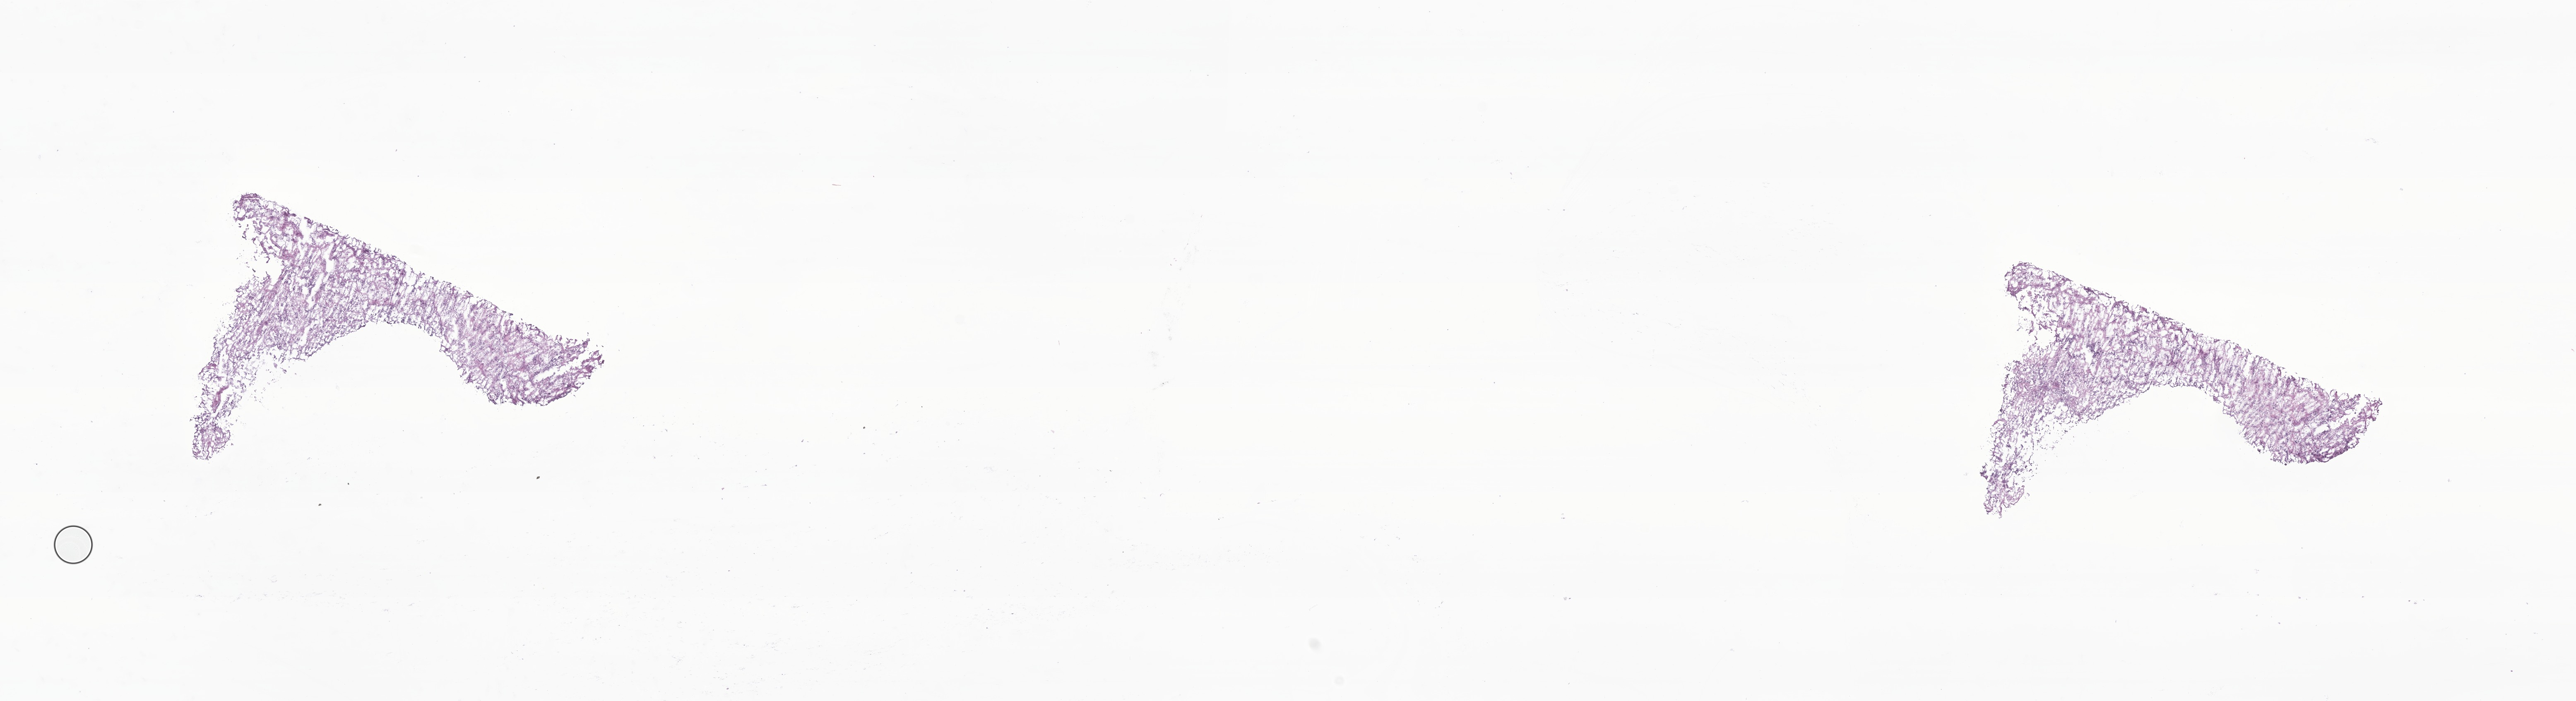
Digitized haematoxylin and eosin-stained section of tumor tissue from the brain, low-resolution overview of the scanned area, about 26.2 x 7.1 mm. Cryosection (OCT / tissue freezing medium). Patient male; age 103 months (8 years 7 months).
Diagnosis: Medulloblastoma, NOS.